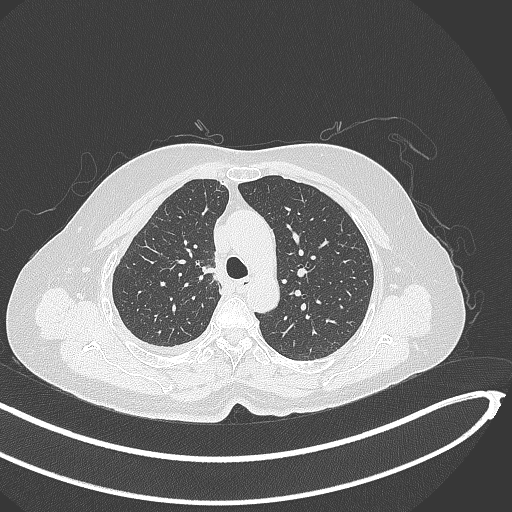
Chest CT, one axial slice; slice 269 of 345 in the series (ordered by position); 120 kVp; lung window (W 1500 / L -600 HU); 1 mm slice thickness; 512 × 512 image matrix, field of view 400 × 400 mm. Female patient, age 64 years. Case-level facts recorded for this patient, not image findings: clinical TNM (as recorded): T1b N0 M1.
Annotated regions visible in this slice (rectangle marked by the reading radiologist):
- lung tumour (recorded histology: adenocarcinoma): bounding box <197,258,222,281> (left, top, right, bottom; pixels)